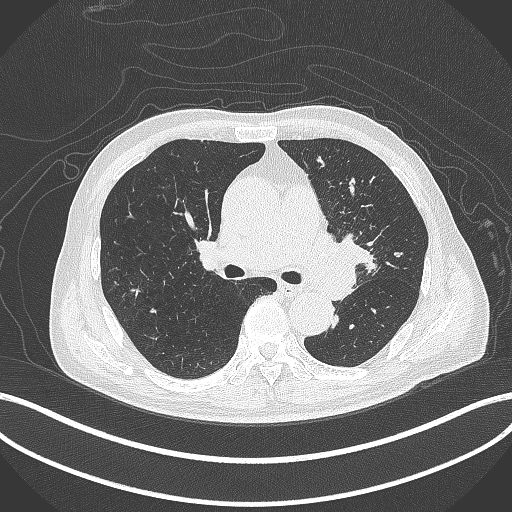
Chest CT, one axial slice; position 259 of 417 along the scan axis; reconstruction kernel B70f; lung window (W 1500 / L -600 HU); 1 mm slice thickness; 512 × 512 image matrix. Male patient, age 77 years. Case-level facts recorded for this patient, not image findings: clinical TNM (as recorded): T3 N1 M0.
Structures marked on this image (bounding box drawn by a radiologist):
- lung tumour (recorded histology: adenocarcinoma): bounding box (x1, y1, x2, y2) in pixels: (311, 228, 375, 297)